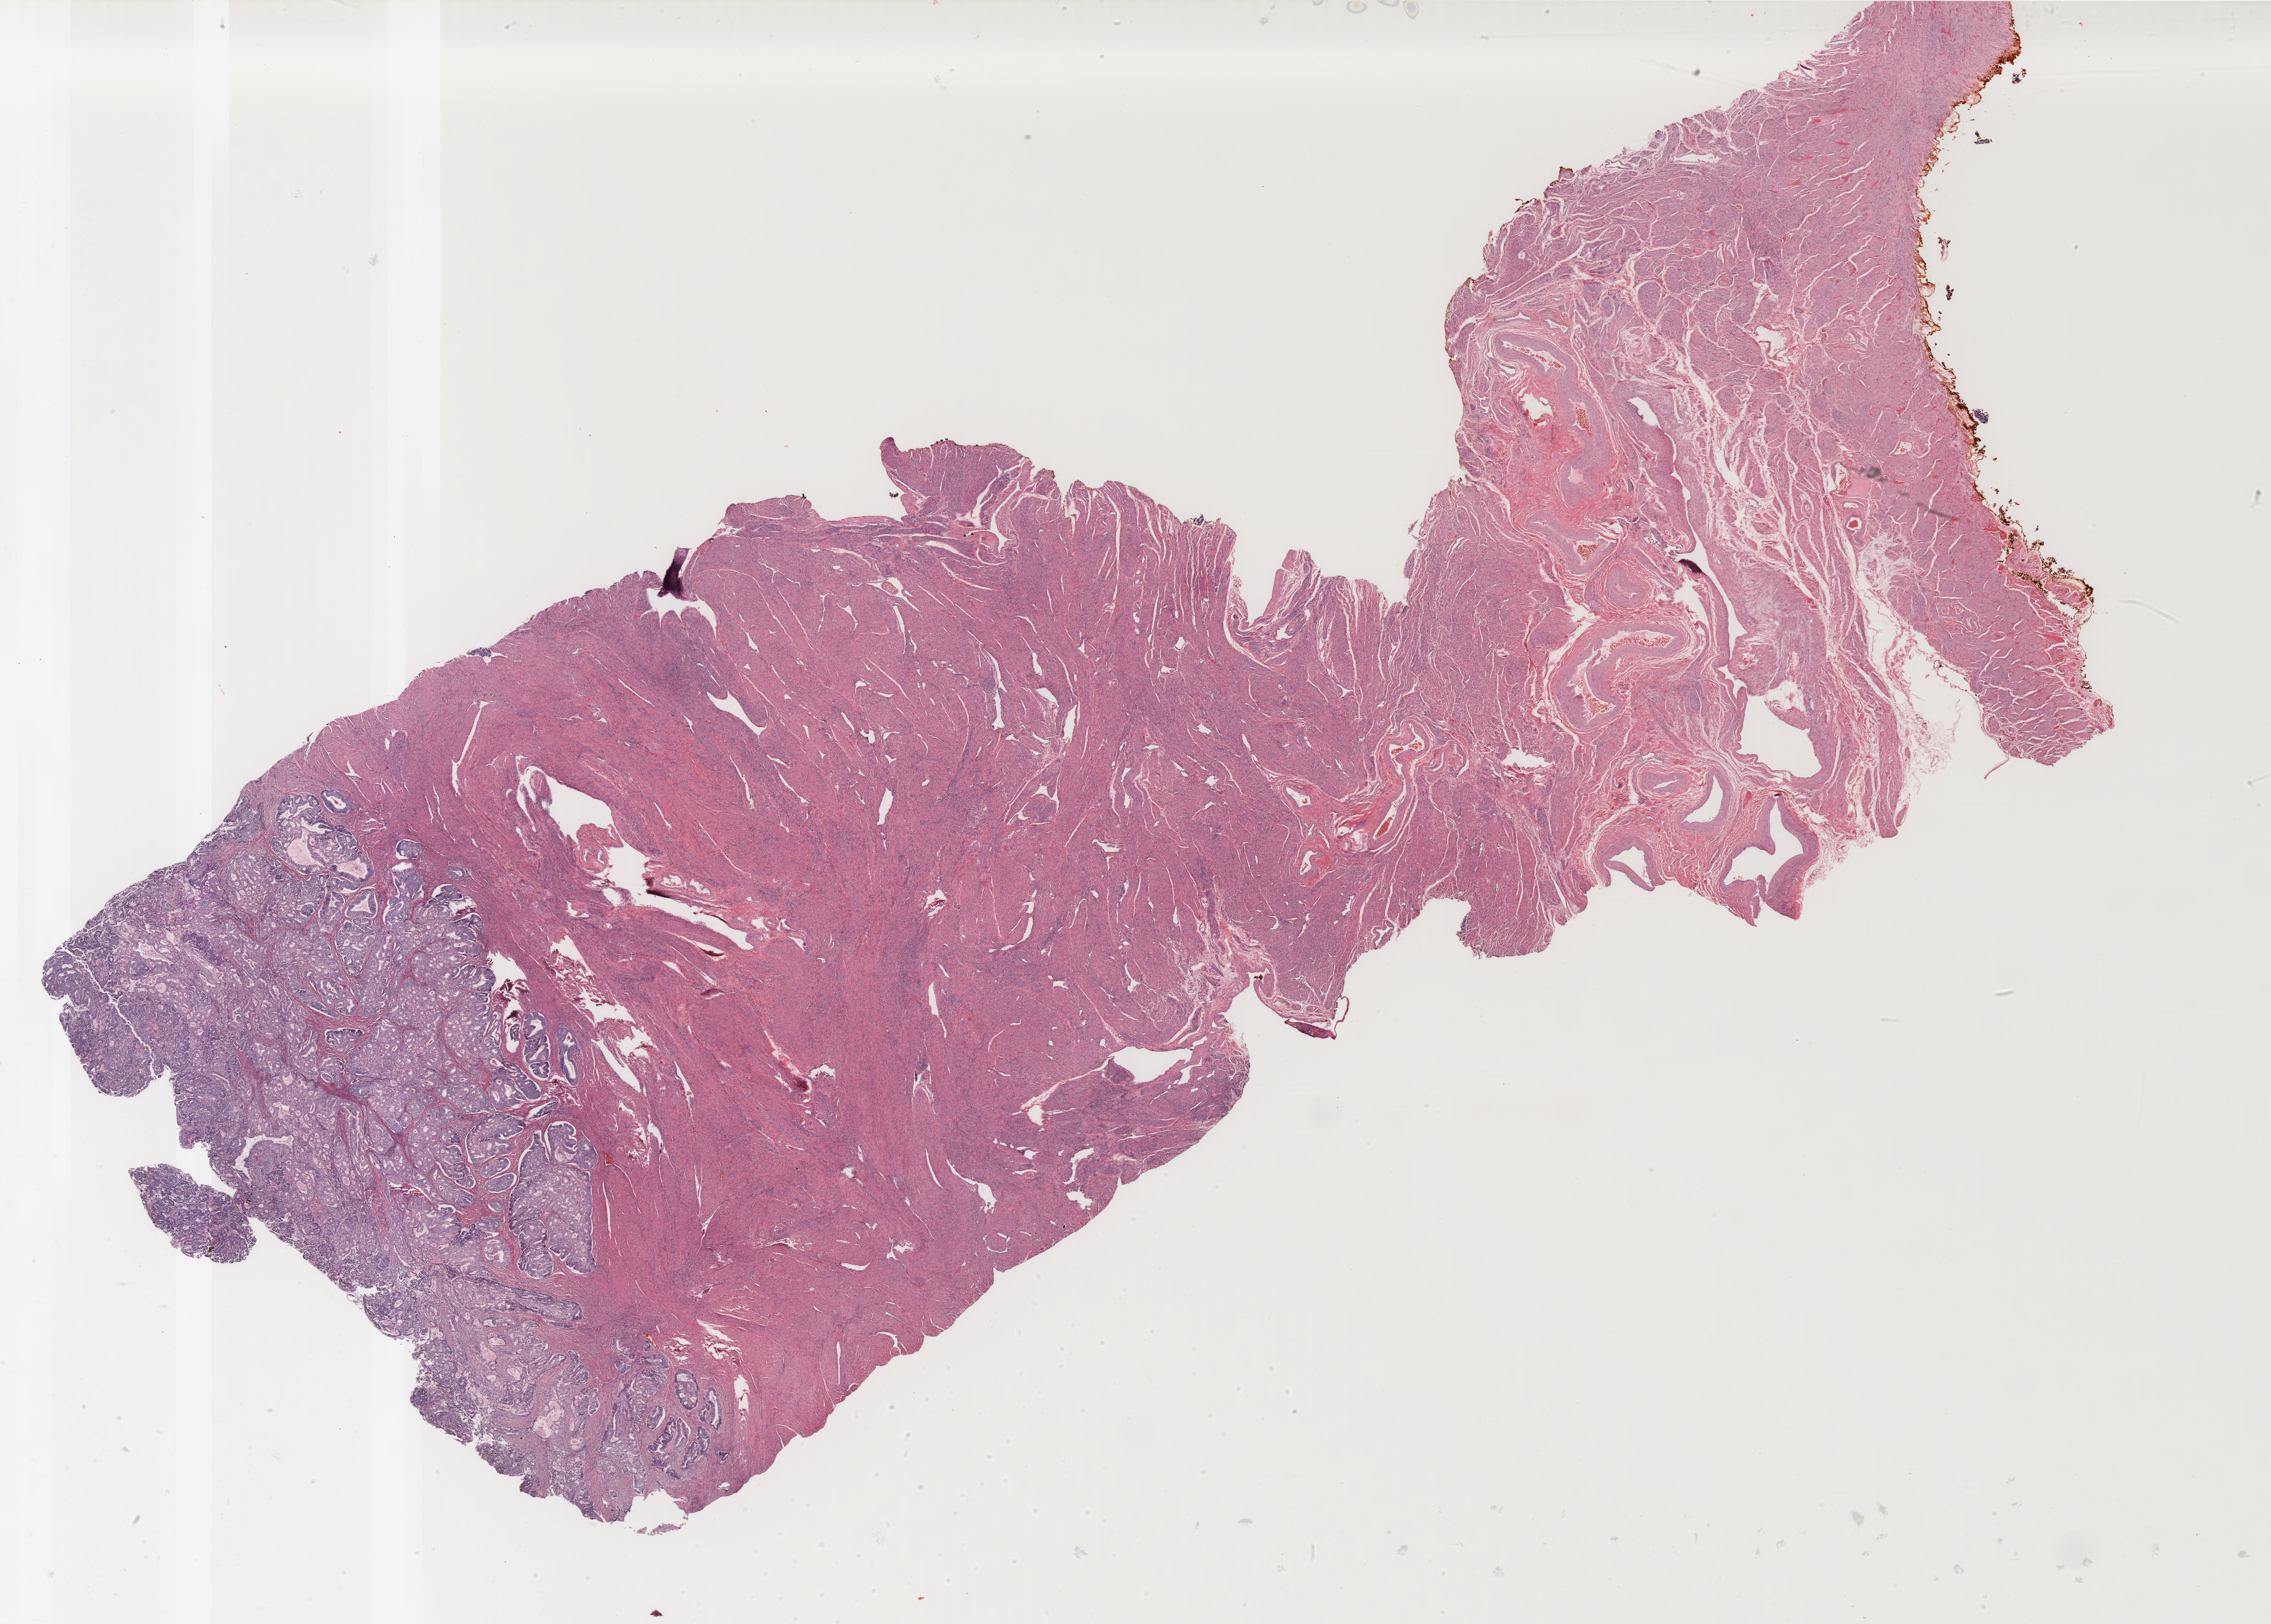
H&E-stained whole-slide image, low-resolution overview of the scanned area, about 30.5 x 21.8 mm (slide scanned at 40x); formalin-fixed paraffin-embedded (FFPE) diagnostic section; sample: primary tumour, uterus. Patient: female, age at initial diagnosis 59 years. Histologic grade: G2 (moderately differentiated).
FIGO stage: IC. Pathologic diagnosis: Endometrioid adenocarcinoma, NOS (endometrium).